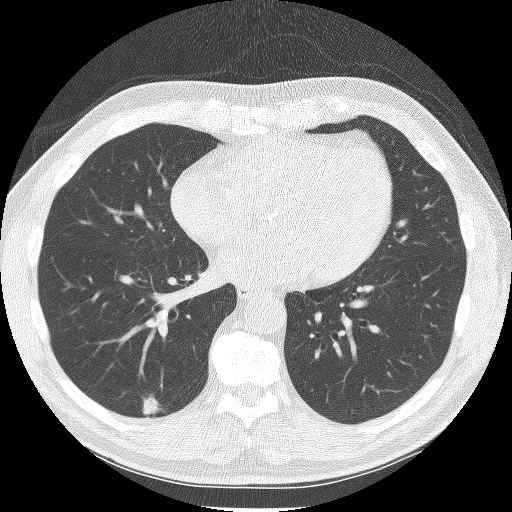
Chest CT (low-dose screening protocol), one axial image. Baseline annual screen. Lung window (W 1500 / L -600 HU). Slice 88 of 150 in the series. Male participant, aged 61 years at enrolment. Current smoker at enrolment.
Lesion marked by an expert reader, bounding box (x1, y1, x2, y2) in pixels: (126, 385, 170, 425). The exam's reader record, not a measurement of the box and not confirmed to be the same lesion: non-calcified nodule or mass ≥4 mm, right lower lobe, 12 × 11 mm, spiculated (stellate) margins, soft tissue attenuation. Official screen result: positive, change unspecified: nodule(s) >= 4 mm or enlarging nodule(s), mass(es), or other non-specific abnormalities suspicious for lung cancer. Participant outcome: lung cancer diagnosed 232 days after this screen — adenocarcinoma, NOS, right lower lobe, moderately differentiated (G2), stage IA (AJCC 6th edition), 9 mm at pathology.